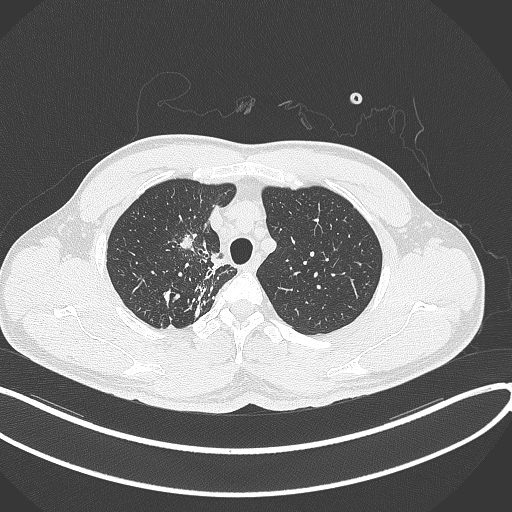
Chest CT, one axial slice. Position 303 of 391 along the scan axis. Reconstruction kernel B70f. Lung window (W 1500 / L -600 HU). 512 × 512 image matrix, field of view 400 × 400 mm. Male patient, age 48 years. Case-level facts recorded for this patient, not image findings: clinical TNM (as recorded): T1c N1 M1.
Outlined on this slice (rectangle marked by the reading radiologist):
- lung tumour (recorded histology: adenocarcinoma): bounding box [x1, y1, x2, y2] px = [171, 228, 202, 267]